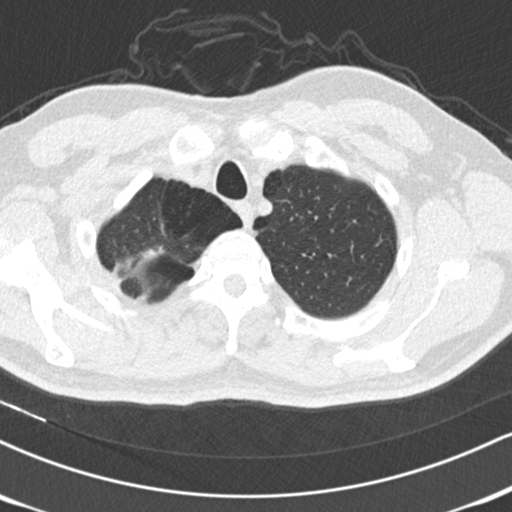
Chest CT (low-dose screening protocol), one axial image, second screening round (one year after baseline), lung window (W 1500 / L -600 HU), standard (soft-tissue) reconstruction kernel (B30f), slice 27 of 179 in the series, 512 × 512 image matrix. Male, age 56 years at enrolment. Former smoker at enrolment.
Expert reader's lesion annotation, box from (x=119, y=235) to (x=177, y=283) px. Screening reader's record for this exam (one nodule recorded; not confirmed to be the boxed lesion): non-calcified nodule or mass ≥4 mm, right upper lobe, 13 × 10 mm, spiculated (stellate) margins, soft tissue attenuation. Official screen result: positive, other. Participant outcome: lung cancer diagnosed 384 days after this screen — adenocarcinoma, NOS, right upper lobe, moderately differentiated (G2), stage IA (AJCC 6th edition), 9 mm at pathology.